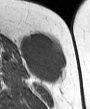
MRI of an extremity soft-tissue mass, one axial slice. Slice 18 of 45 in the series (ordered by position). MR volume resampled by the dataset authors to the PET/CT grid (not the native acquisition matrix). 3.27 mm slice thickness. 90 × 109 image matrix, field of view 88 × 106 mm. Female patient. Case-level facts recorded for this patient, not image findings: histological type: leiomyosarcoma; grade: intermediate; site of the primary tumour: parascapusular.
Outlined on this slice (expert contour drawn on MRI and transferred to this co-registered scan by the dataset authors):
- gross tumour volume including surrounding oedema: bounding box (x1, y1, x2, y2) in pixels: (19, 32, 66, 83)
- gross tumour volume (mass): (19, 32, 66, 83)